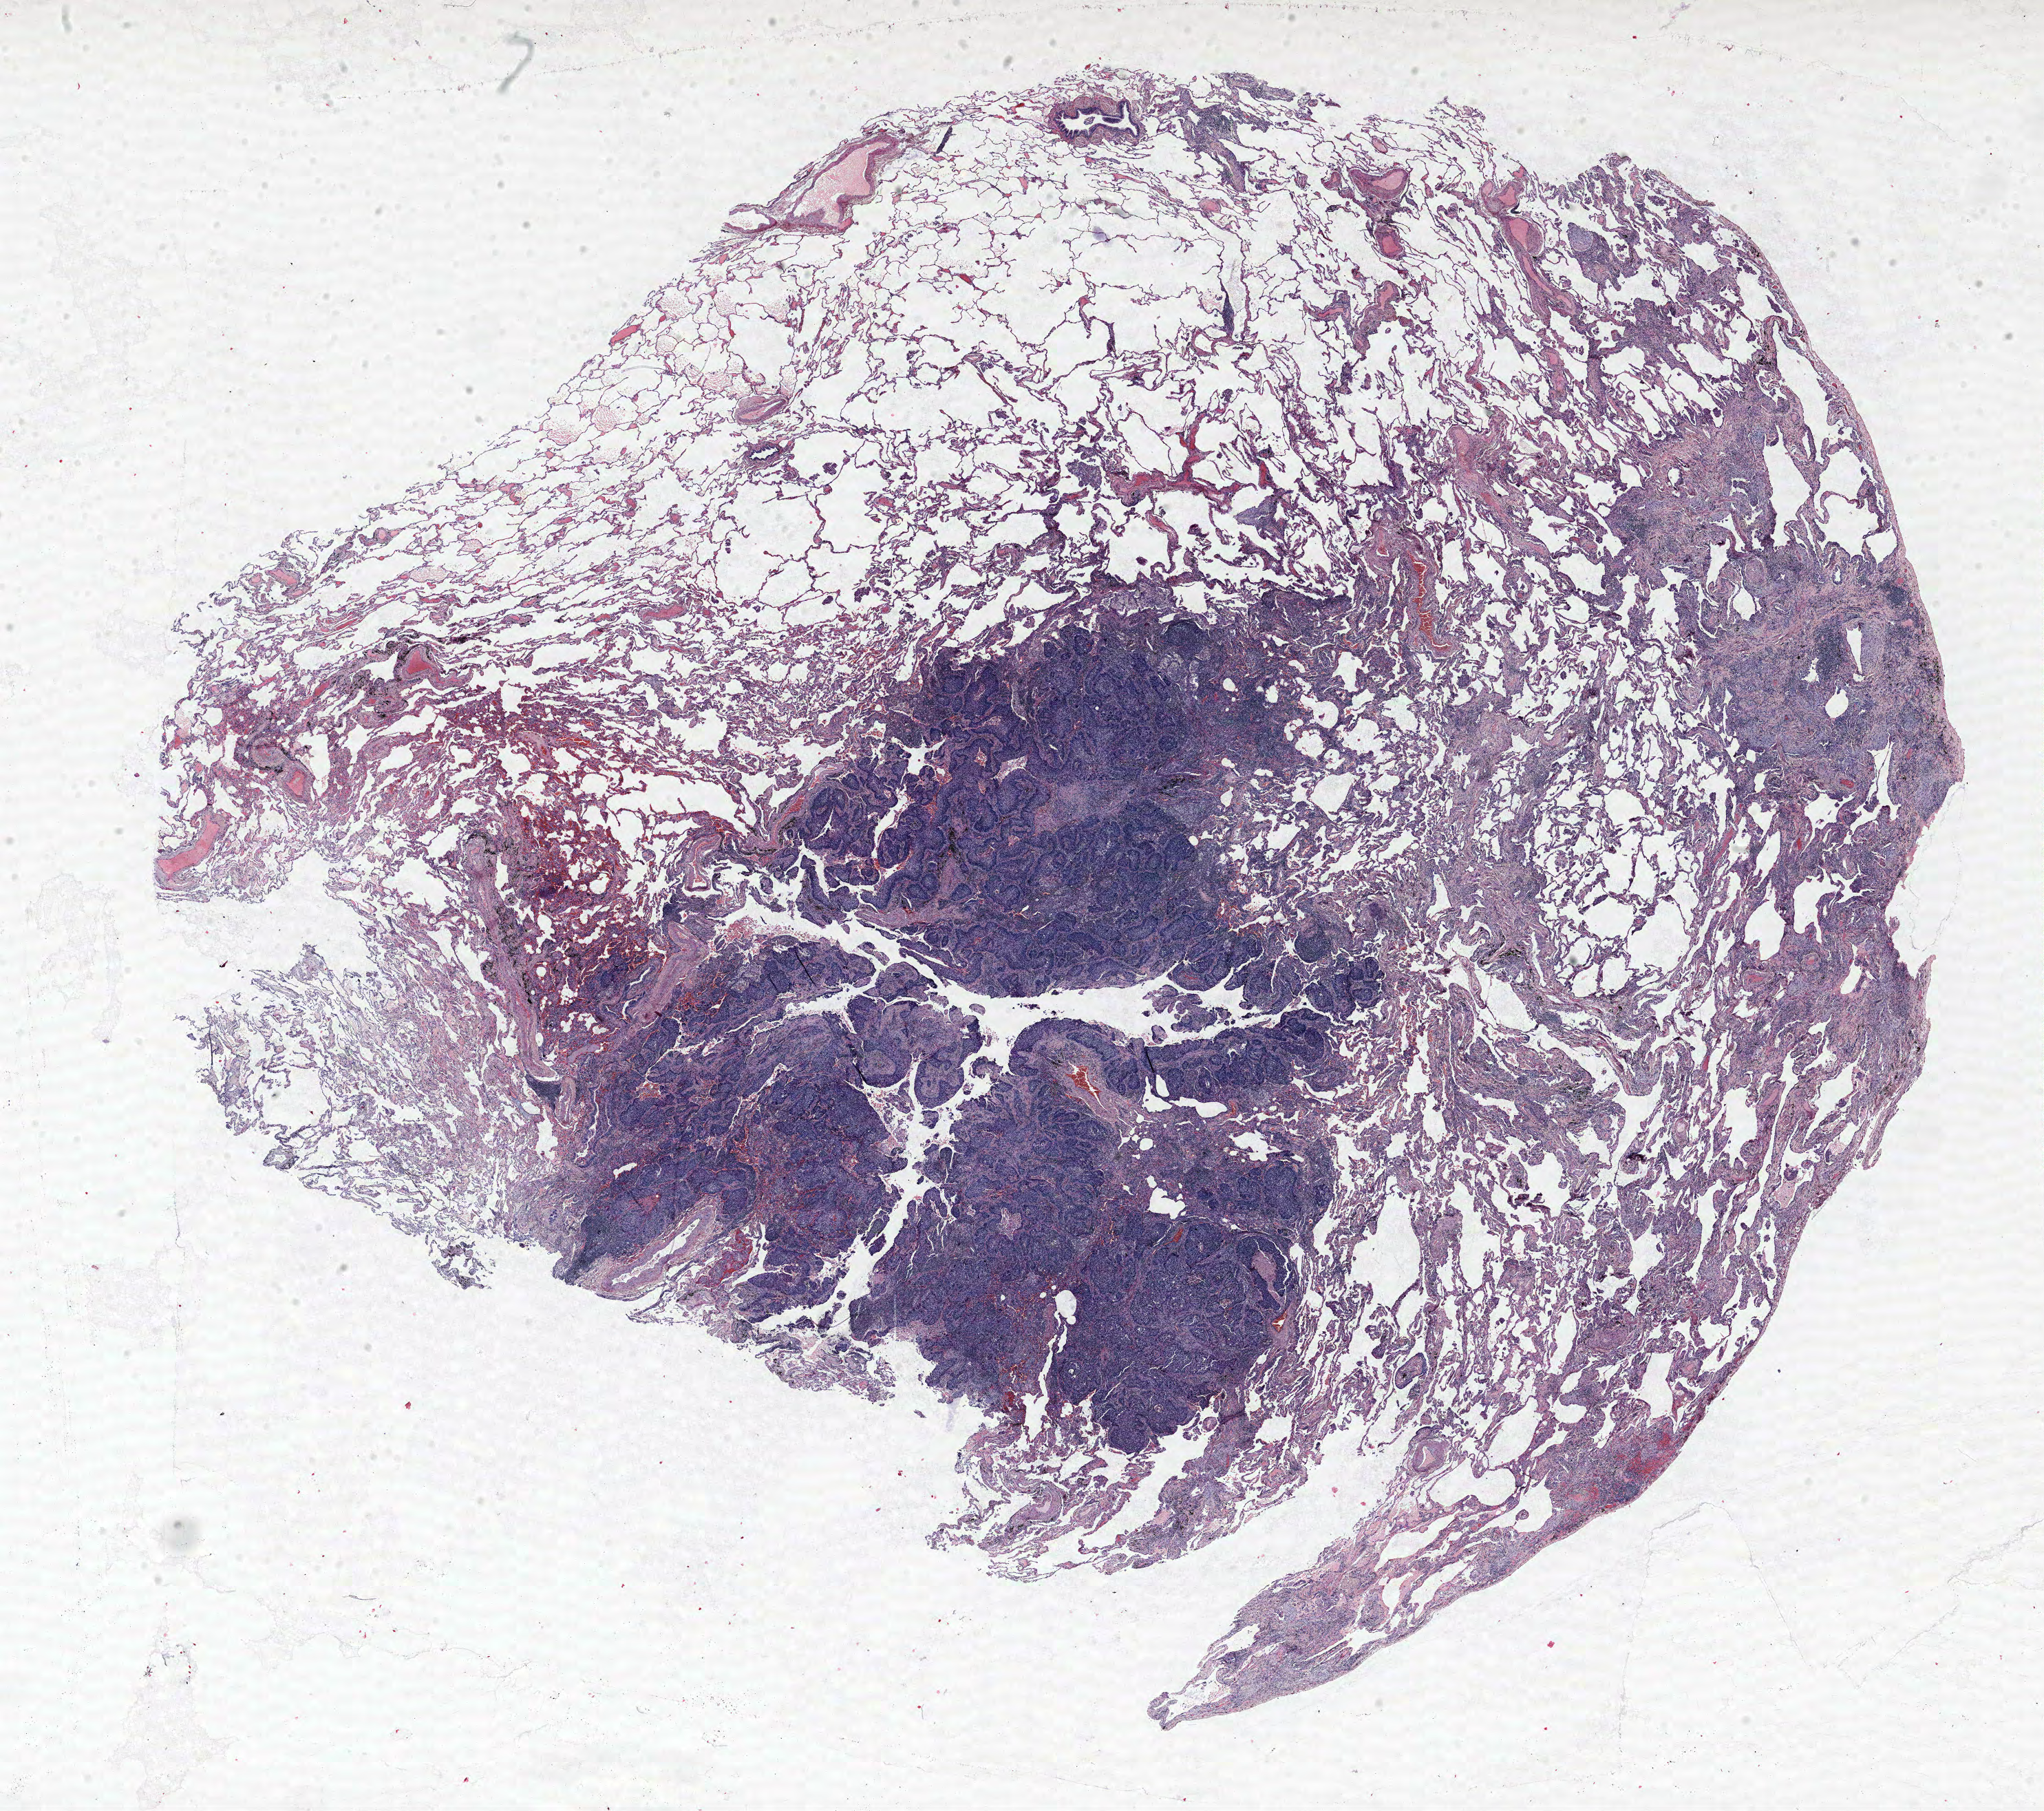
Whole-slide histology image, H&E — a low-resolution overview of the entire scanned area, about 23.8 x 21.1 mm (slide scanned at 40x), formalin-fixed paraffin-embedded (FFPE) section, lung. Male, age 58 at enrolment. Former smoker at enrolment. Grade: poorly differentiated (G3).
Tumour size (pathology): 18 mm. ICD-O-3 topography: upper lobe of lung (C34.1). Primary tumour location (clinical record): right upper lobe. Stage (AJCC 6th edition): IA. Participant's lung-cancer diagnosis: Squamous cell carcinoma, NOS (ICD-O-3 8070/3).